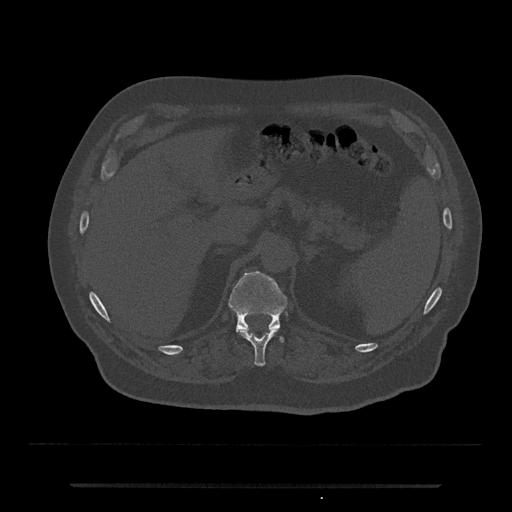
CT including the spine, one axial slice. Slice 620 of 797 in the series (ordered by position). 120 kVp. Bone window (W 1800 / L 400 HU). 0.5 mm slice thickness. 512 × 512 image matrix, field of view 434 × 434 mm. Patient: male, 80 years. From the clinical record (not read from this slice): primary cancer: prostate.
Annotated regions visible in this slice (semi-automatically segmented with operator editing):
- T11 vertebra: bounding box <239,329,277,367> (left, top, right, bottom; pixels)
- T12 vertebra: <228,270,288,344>